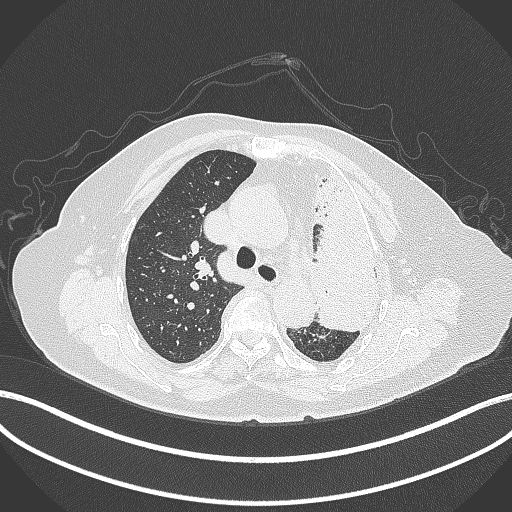
Chest CT, one axial slice. Slice 278 of 399 in the series (ordered by position). Reconstruction kernel B70f. Lung window (W 1500 / L -600 HU). 1 mm slice thickness. 512 × 512 image matrix, field of view 400 × 400 mm. Patient: female, 75 years. From the clinical record (not read from this slice): clinical TNM (as recorded): T3 N3 M1.
Outlined on this slice (rectangle marked by the reading radiologist):
- lung tumour (recorded histology: adenocarcinoma): box from (x=308, y=162) to (x=386, y=331) px